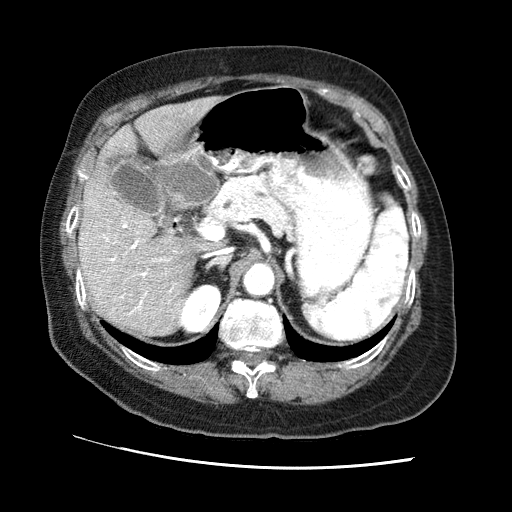
Contrast-enhanced abdominal CT (liver protocol), one axial slice. Position 36 of 65 along the scan axis. Reconstruction kernel STANDARD. 120 kVp. Soft-tissue window (W 400 / L 40 HU). 2.5 mm slice thickness. 512 × 512 image matrix, field of view 340 × 340 mm. Case-level facts recorded for this patient, not image findings: diagnosis: hepatocellular carcinoma (patient treated with transarterial chemoembolisation; whether this scan precedes or follows treatment is not stated here); TNM stage (as recorded): Stage-II; Child-Pugh class: A; tumour differentiation: no biopsy; tumour nodularity: multinodular.
Outlined on this slice (semi-automatically segmented with operator editing):
- liver parenchyma outside the tumour (the mass and vessels are separate outlines, so this box may not span the whole liver): box from (x=78, y=96) to (x=221, y=336) px
- liver vessels: (x=86, y=222)–(x=172, y=314)